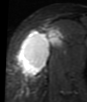
MRI of an extremity soft-tissue mass, one axial slice; position 30 of 48 along the scan axis; STIR; MR volume resampled by the dataset authors to the PET/CT grid (not the native acquisition matrix); 3.27 mm slice thickness; 87 × 102 image matrix, field of view 85 × 100 mm. Female patient. Case-level facts recorded for this patient, not image findings: histological type: synovial sarcoma; grade: intermediate; site of the primary tumour: right thigh.
Annotated regions visible in this slice (expert contour drawn on MRI and transferred to this co-registered scan by the dataset authors):
- gross tumour volume including surrounding oedema: bounding box <17,27,62,76> (left, top, right, bottom; pixels)
- gross tumour volume (mass): <19,29,62,76>